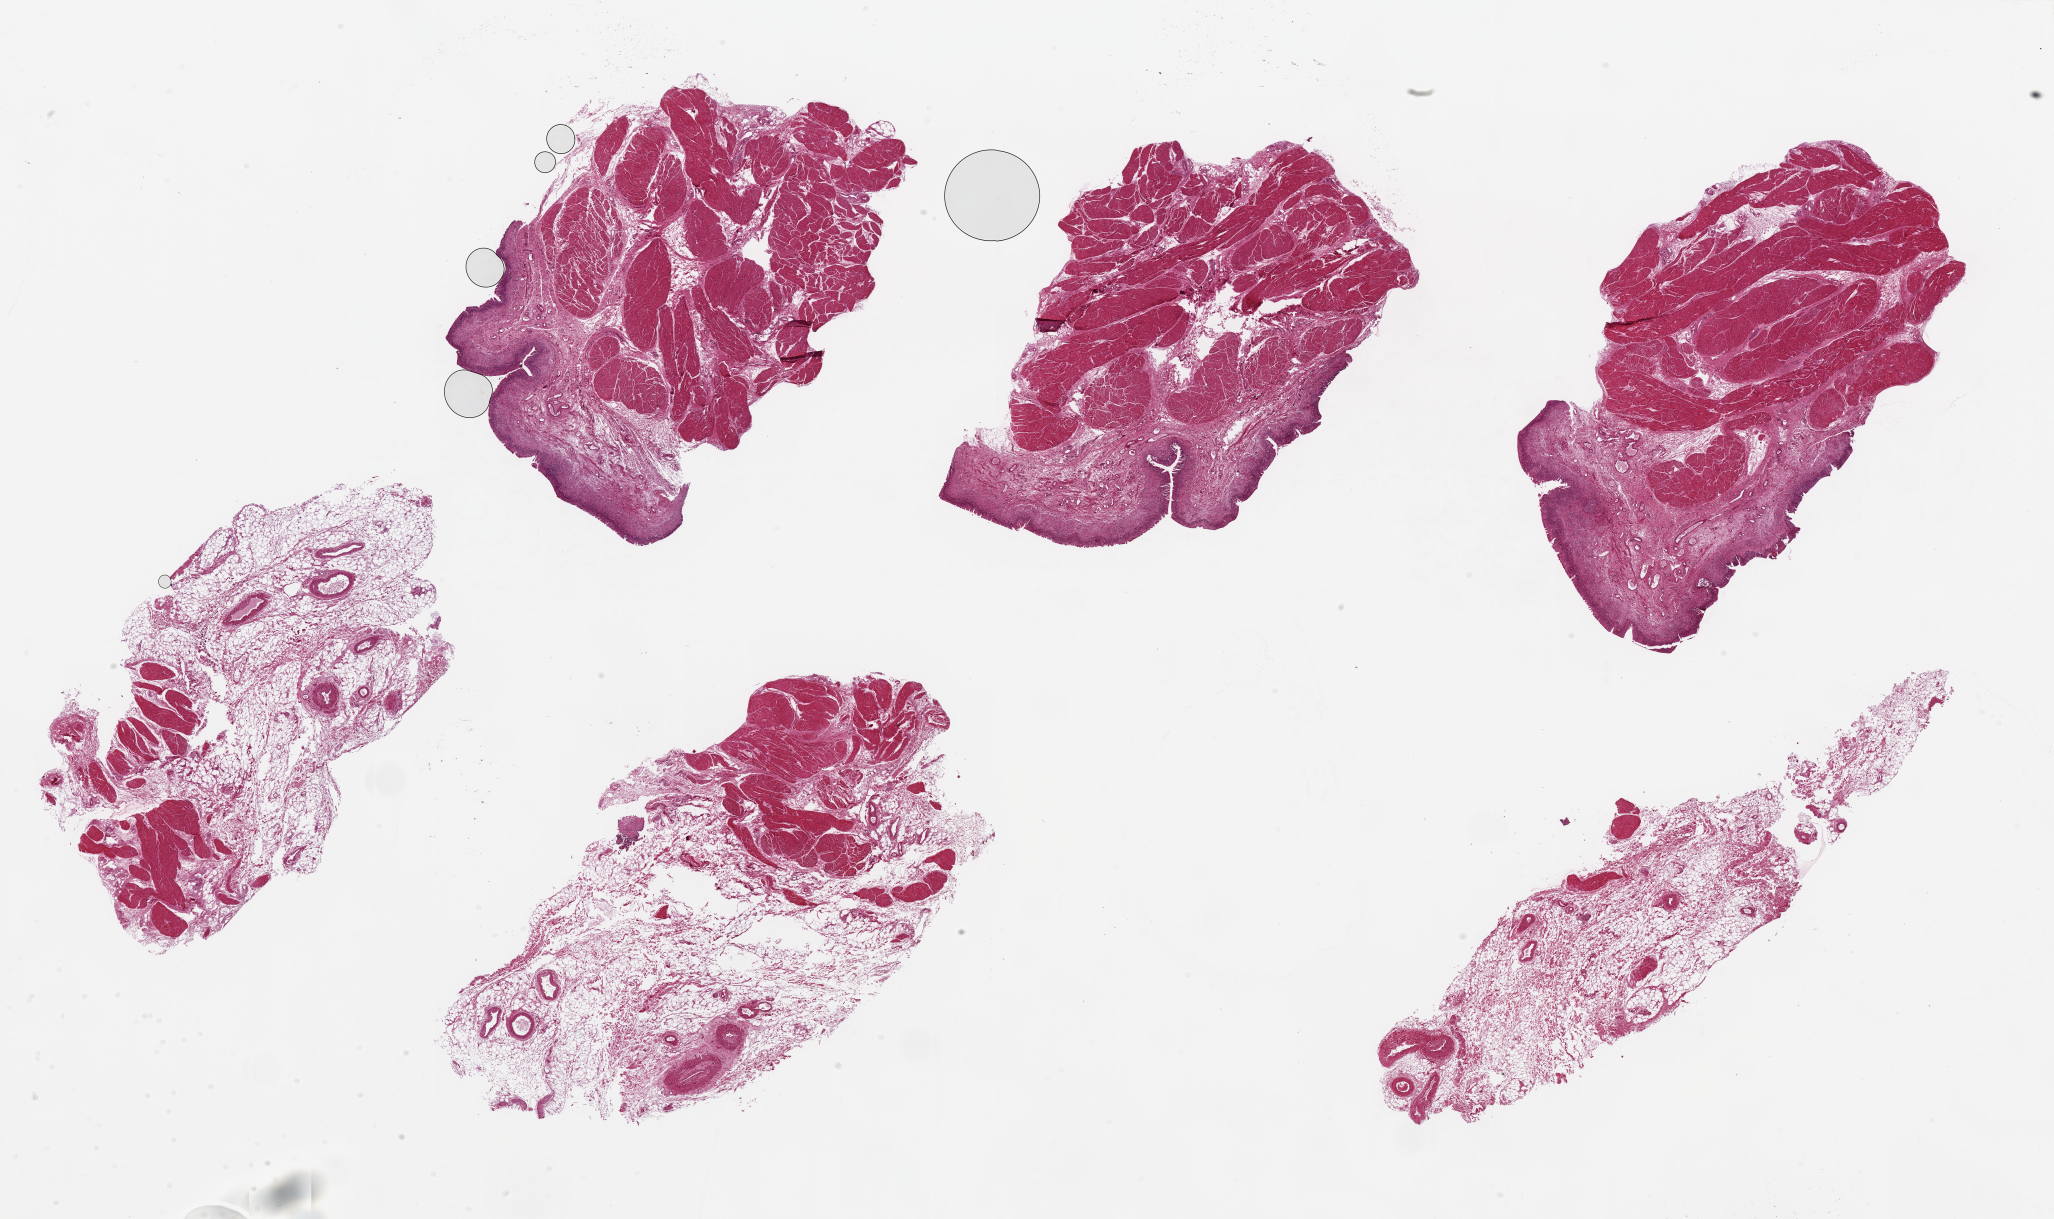
Haematoxylin and eosin whole-slide image — low-resolution overview of the scanned area, about 32.5 x 19.3 mm (from a 20x scan); PAXgene-fixed, paraffin-embedded tissue; sampled site (target tissue): urinary bladder; donor tissue sample. Female donor.
Reviewer comment on this tissue sample: 6 pieces up to 8x5mm; 3 have good mucosa, 3 have no mucosa, but outer muscle and abundant adipose (up to 5x5 mm).